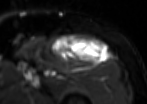
MRI of an extremity soft-tissue mass, one axial slice; position 72 of 85 along the scan axis; T2-weighted fat-saturated; MR volume resampled by the dataset authors to the PET/CT grid (not the native acquisition matrix); 3.27 mm slice thickness; 147 × 104 image matrix. Male patient. Case-level facts recorded for this patient, not image findings: histological type: extraskeletal osteosarcoma; grade: high; site of the primary tumour: thigh.
Annotated regions visible in this slice (expert contour drawn on MRI and transferred to this co-registered scan by the dataset authors):
- gross tumour volume (mass): bounding box [x1, y1, x2, y2] px = [51, 35, 107, 65]